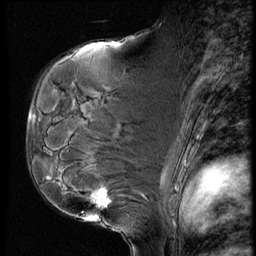
Breast MRI (dynamic contrast-enhanced), one sagittal slice. Dynamic contrast-enhanced series, image 2 of 4 at this slice position (ordered by acquisition). 1.5 T. TE 4.2 ms, TR 9 ms. 2.5 mm slice thickness. 256 × 256 image matrix, field of view 180 × 180 mm. Female patient, age 50 years. From the clinical record (not read from this slice): setting: breast cancer imaged before/during neoadjuvant chemotherapy; receptor status: HR-positive, HER2-negative.
Outlined on this slice (semi-automatic segmentation, software-assisted and operator-edited):
- analysis volume of interest (the breast-tissue region the enhancement analysis was run in; not a lesion): box from (x=48, y=109) to (x=135, y=230) px
- tumour enhancement mask (voxels above the 140 % enhancement threshold inside the analysis volume of interest): (x=92, y=192)–(x=109, y=205)